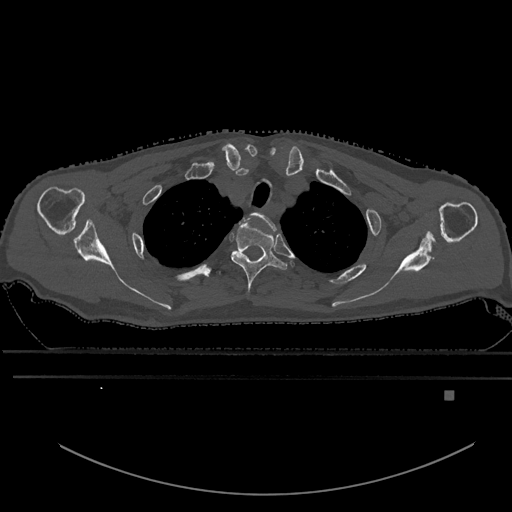
CT including the spine, one axial slice. Position 494 of 969 along the scan axis. Bone window (W 1800 / L 400 HU). 0.5 mm slice thickness. 512 × 512 image matrix, field of view 456 × 456 mm. Patient: male, 82 years. From the clinical record (not read from this slice): primary cancer: prostate.
Outlined on this slice (semi-automatic segmentation, software-assisted and operator-edited):
- T1 vertebra: bounding box (x1, y1, x2, y2) in pixels: (252, 213, 276, 230)
- T2 vertebra: (231, 220, 288, 295)
- T3 vertebra: (216, 271, 221, 275)